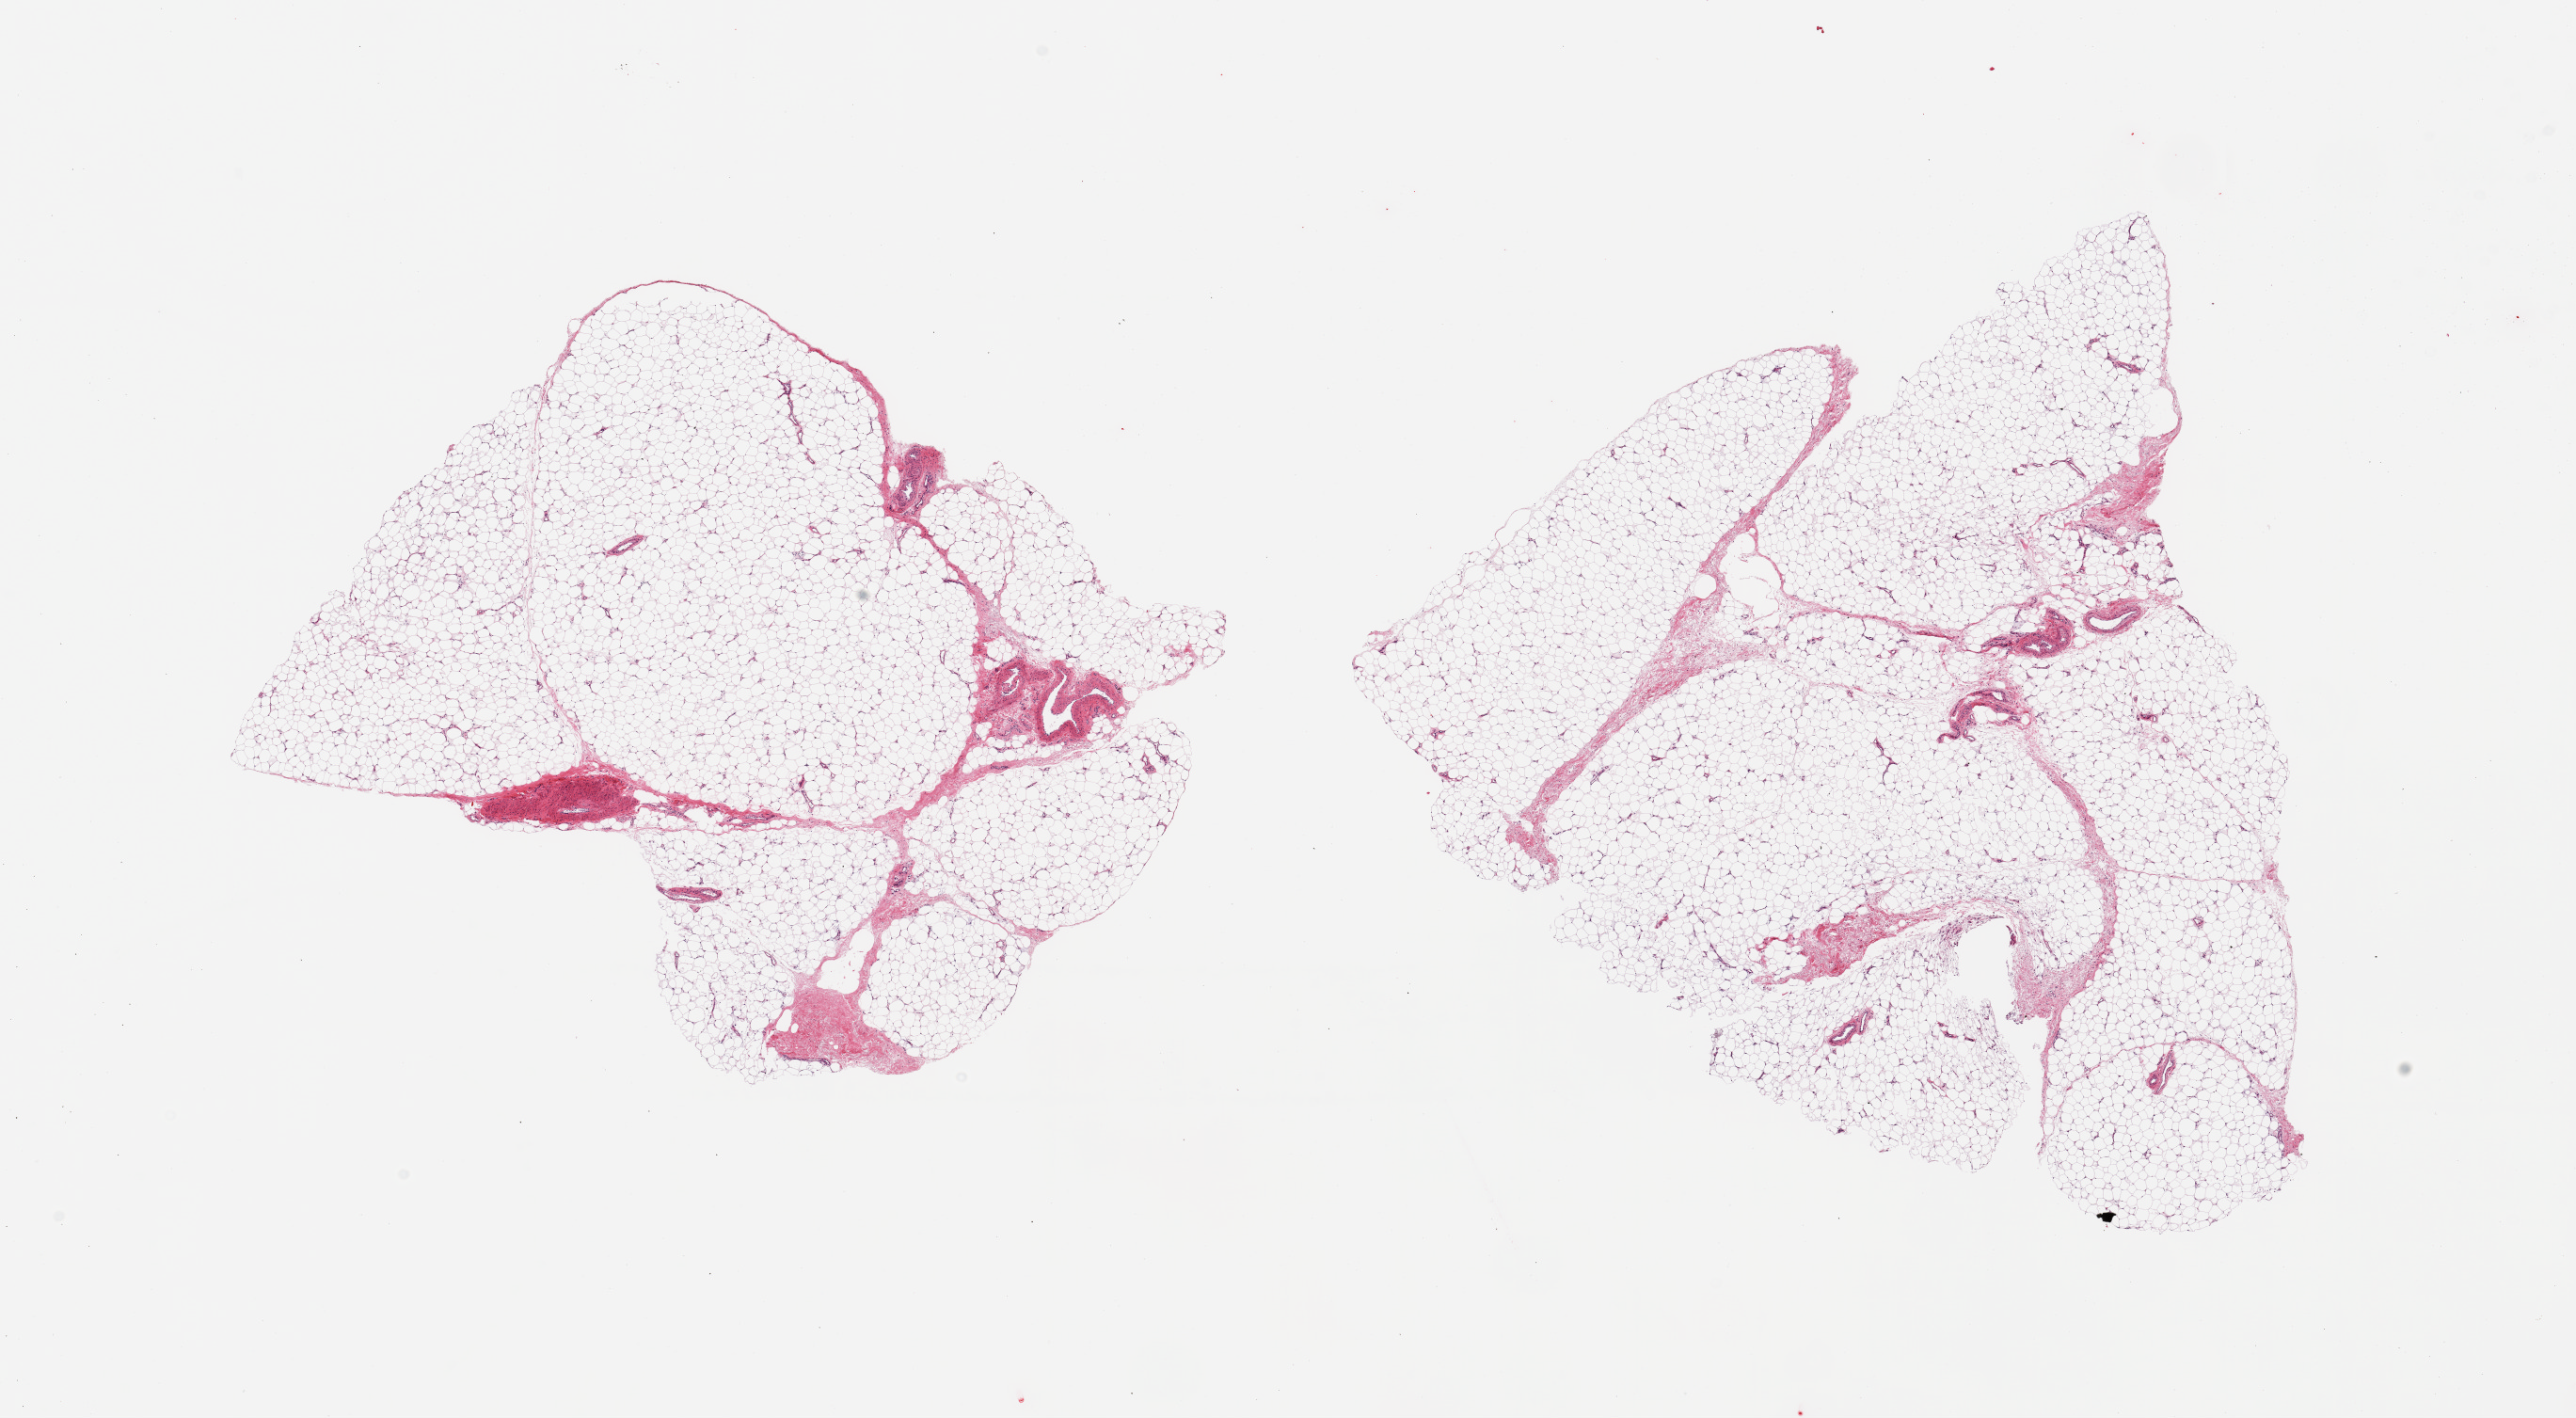
Digitized hematoxylin and eosin (H&E)-stained section — shown as a low-resolution overview of the whole scanned area (about 21.7 x 11.9 mm, from a 20x scan), PAXgene-fixed paraffin-embedded (PFPE) section, sampled site (target tissue): adipose tissue, donor tissue sample.
* pathologist's review note for this sample: 2 pieces; 5% fibrovascular content